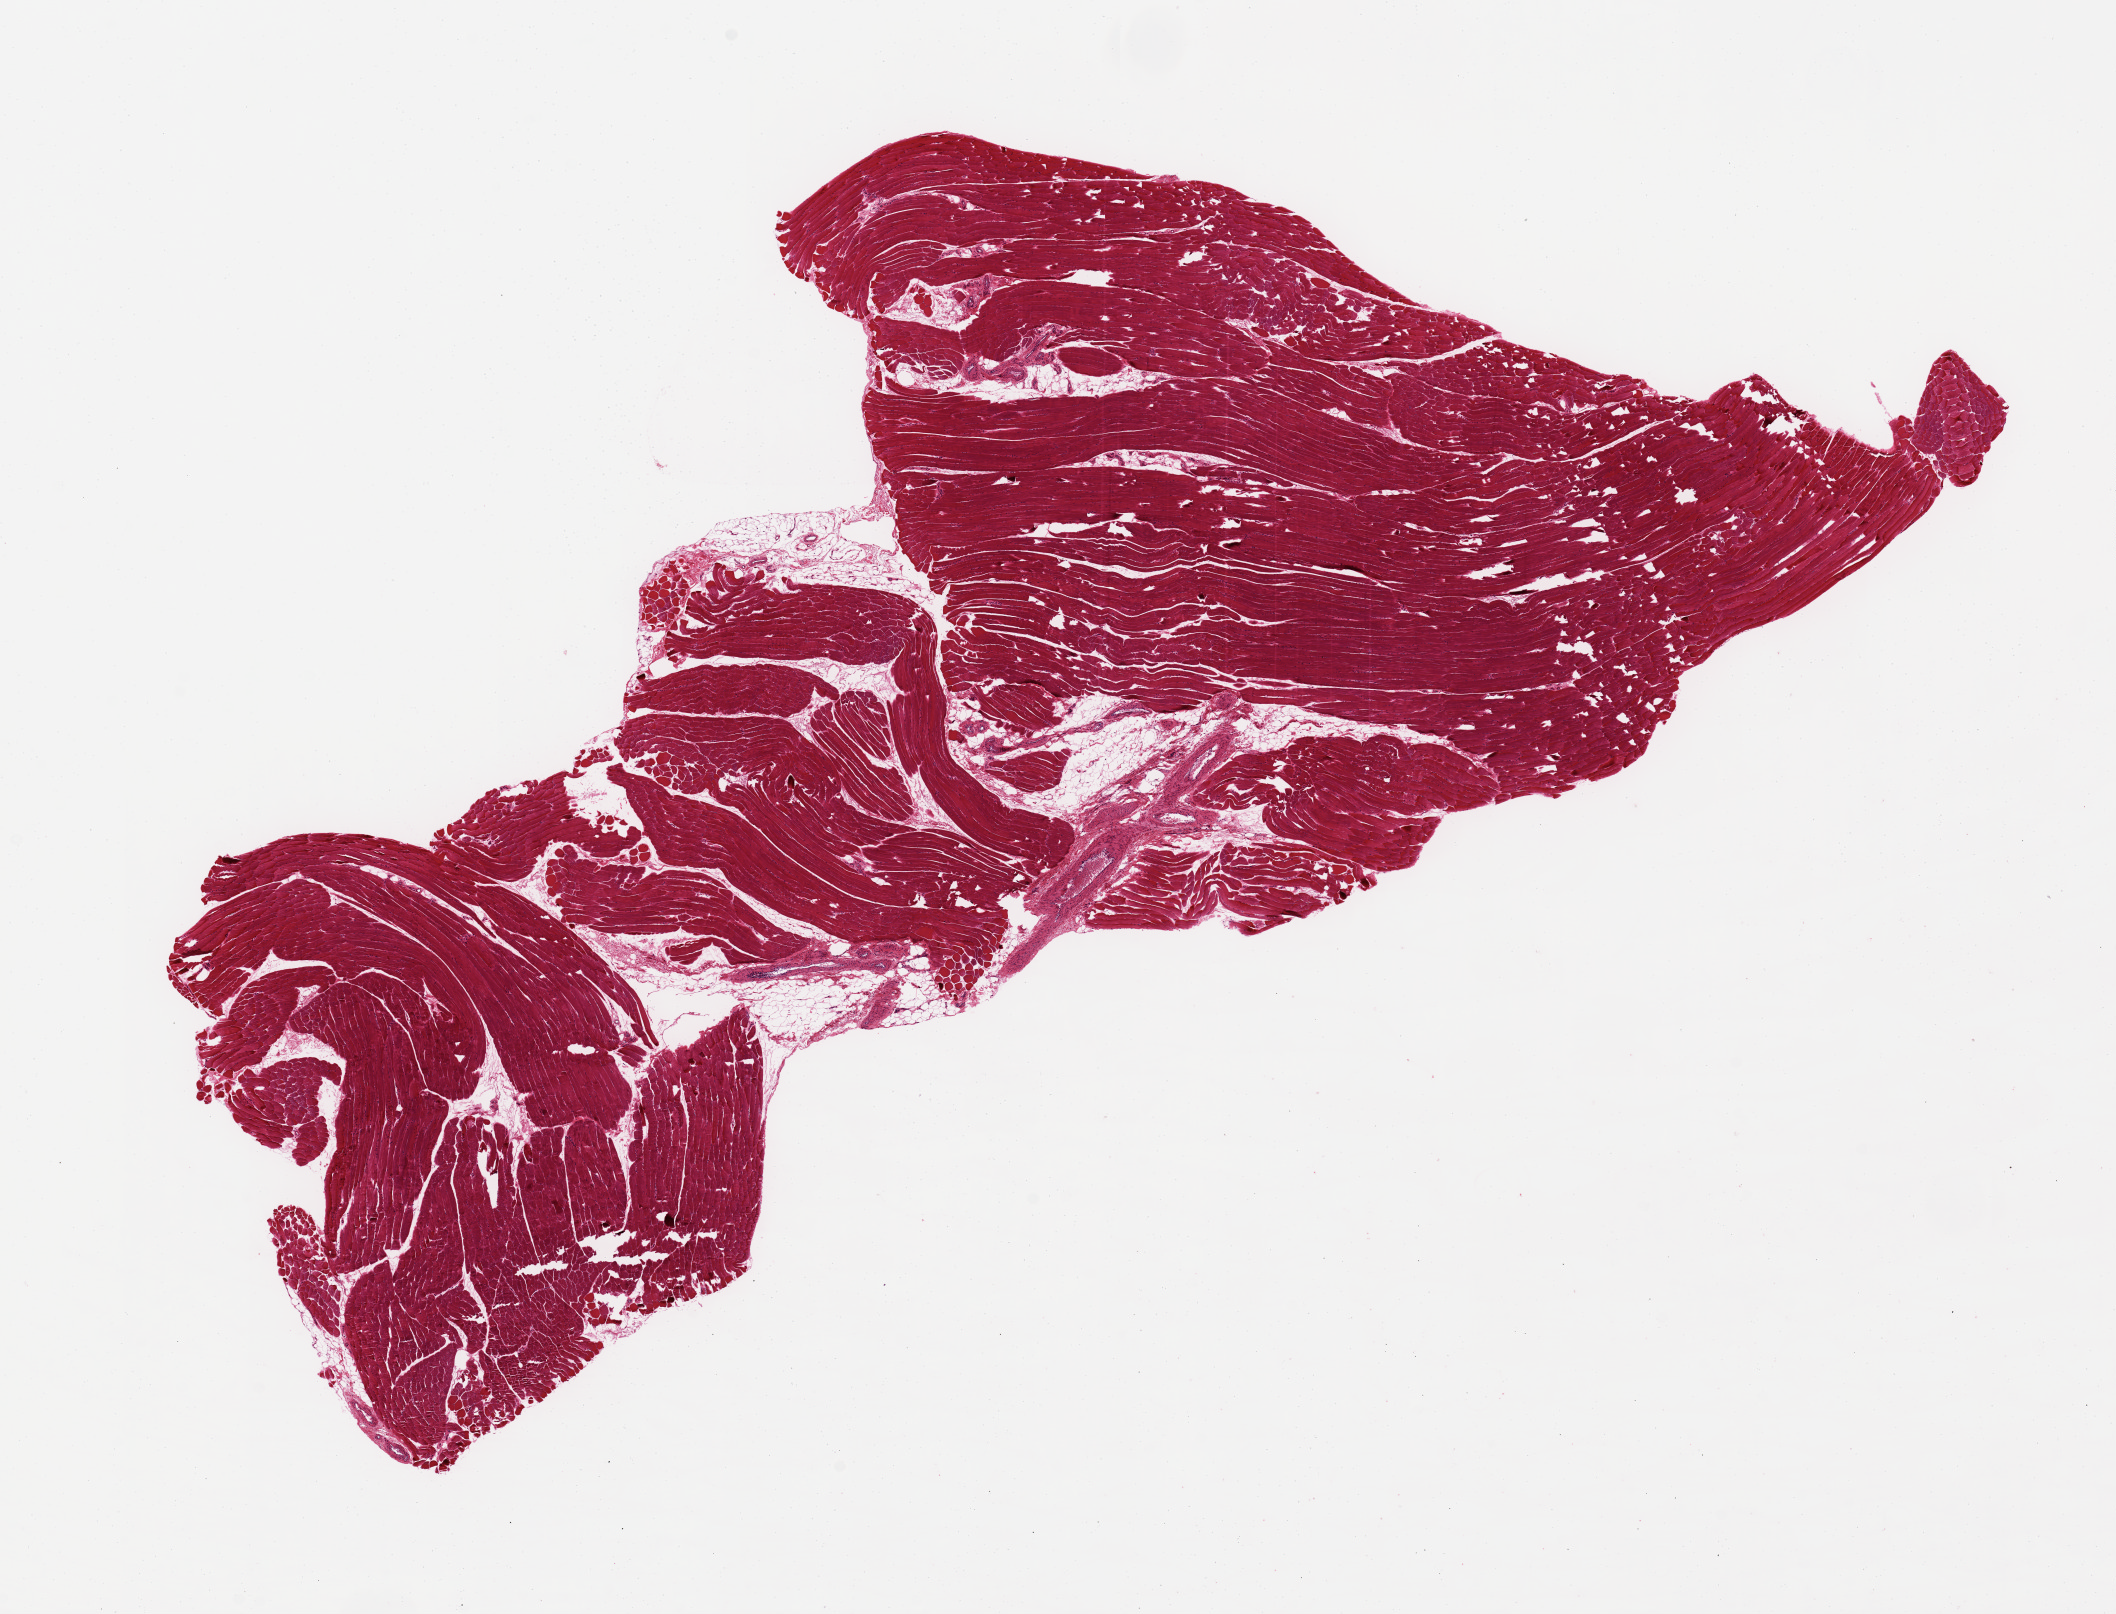
H&E whole-slide image, a low-resolution overview of the entire scanned area, about 16.7 x 12.8 mm (slide scanned at 20x), PAXgene-fixed paraffin-embedded (PFPE) section, section of skeletal muscle (target tissue), tissue donor sample. Donor: male.
- review note (as recorded): 0-1. 12x7mm specimen